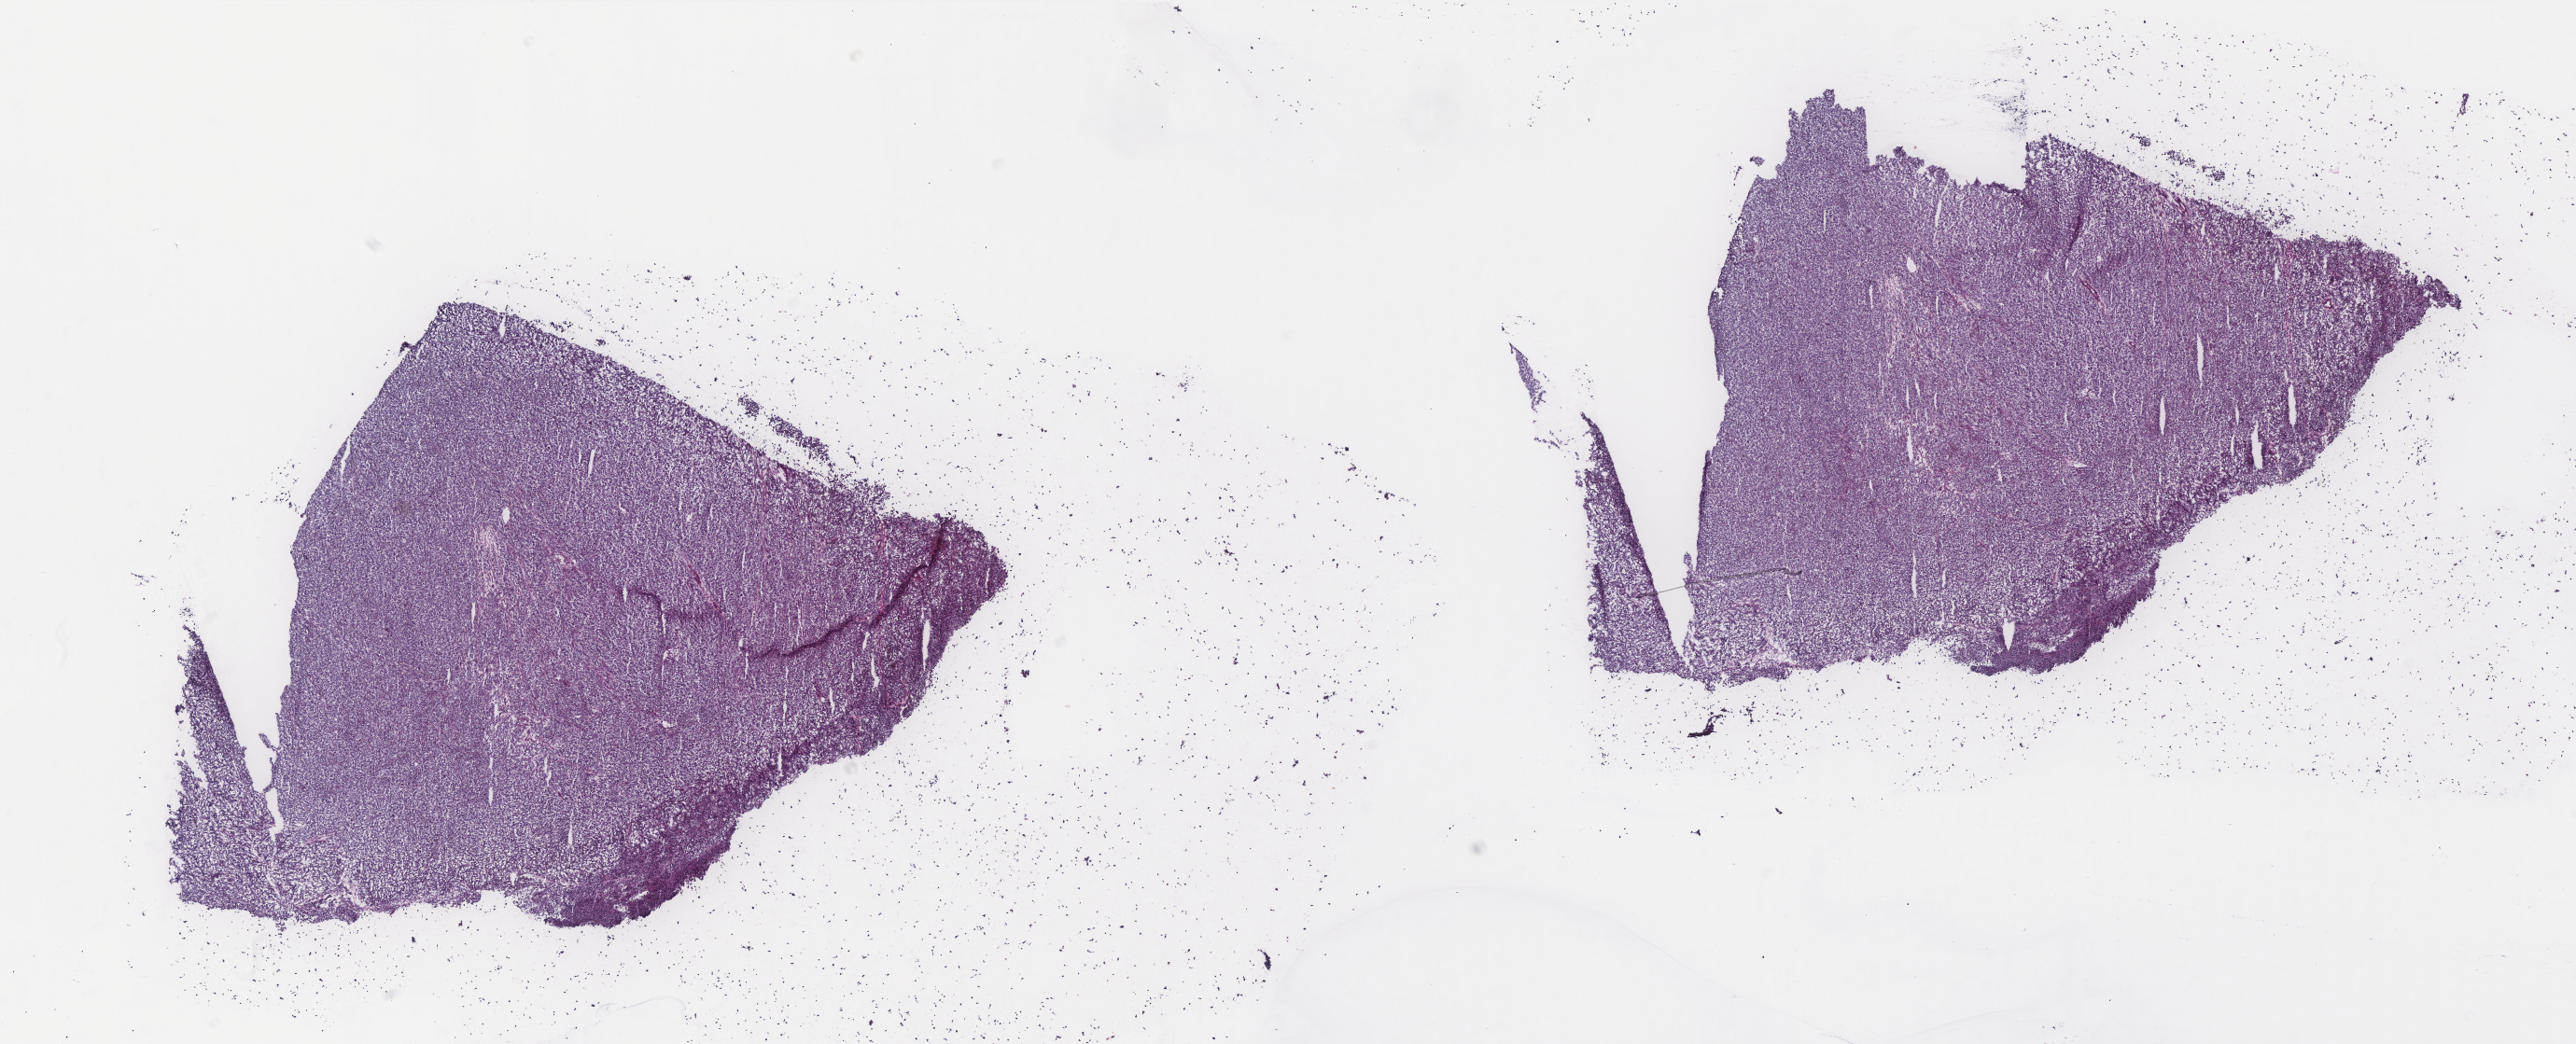
Whole-slide histology image, Hematoxylin and eosin (H&E) stained, whole scanned area (about 22.1 x 9.0 mm, from a 40x scan) shown as a low-resolution overview; frozen section from the top of the tissue portion; metastatic tumour sample, sampled site not recorded. Patient: female, age at initial diagnosis 37 years. Slide review estimates, as recorded: tumour cells 95%, tumour nuclei 95%.
This section: metastatic tumour tissue. Patient diagnosis: Malignant melanoma, NOS.